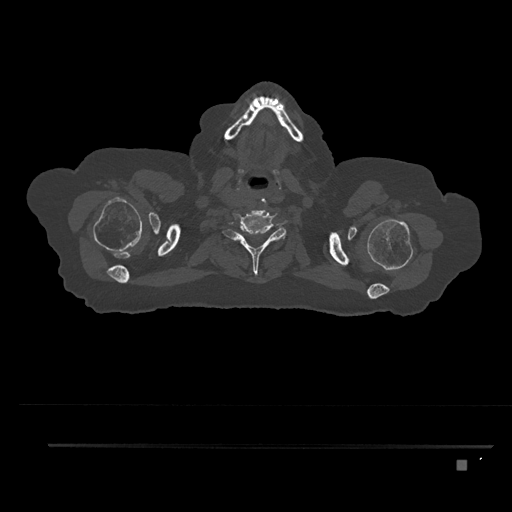
CT including the spine, one axial slice. Position 732 of 797 along the scan axis. 120 kVp. Bone window (W 1800 / L 400 HU). 0.5 mm slice thickness. 512 × 512 image matrix, field of view 437 × 437 mm. Patient: female, 76 years. Case-level facts recorded for this patient, not image findings: primary cancer: lung.
Annotated regions visible in this slice (semi-automatically segmented with operator editing):
- T1 vertebra: box from (x=242, y=244) to (x=251, y=254) px